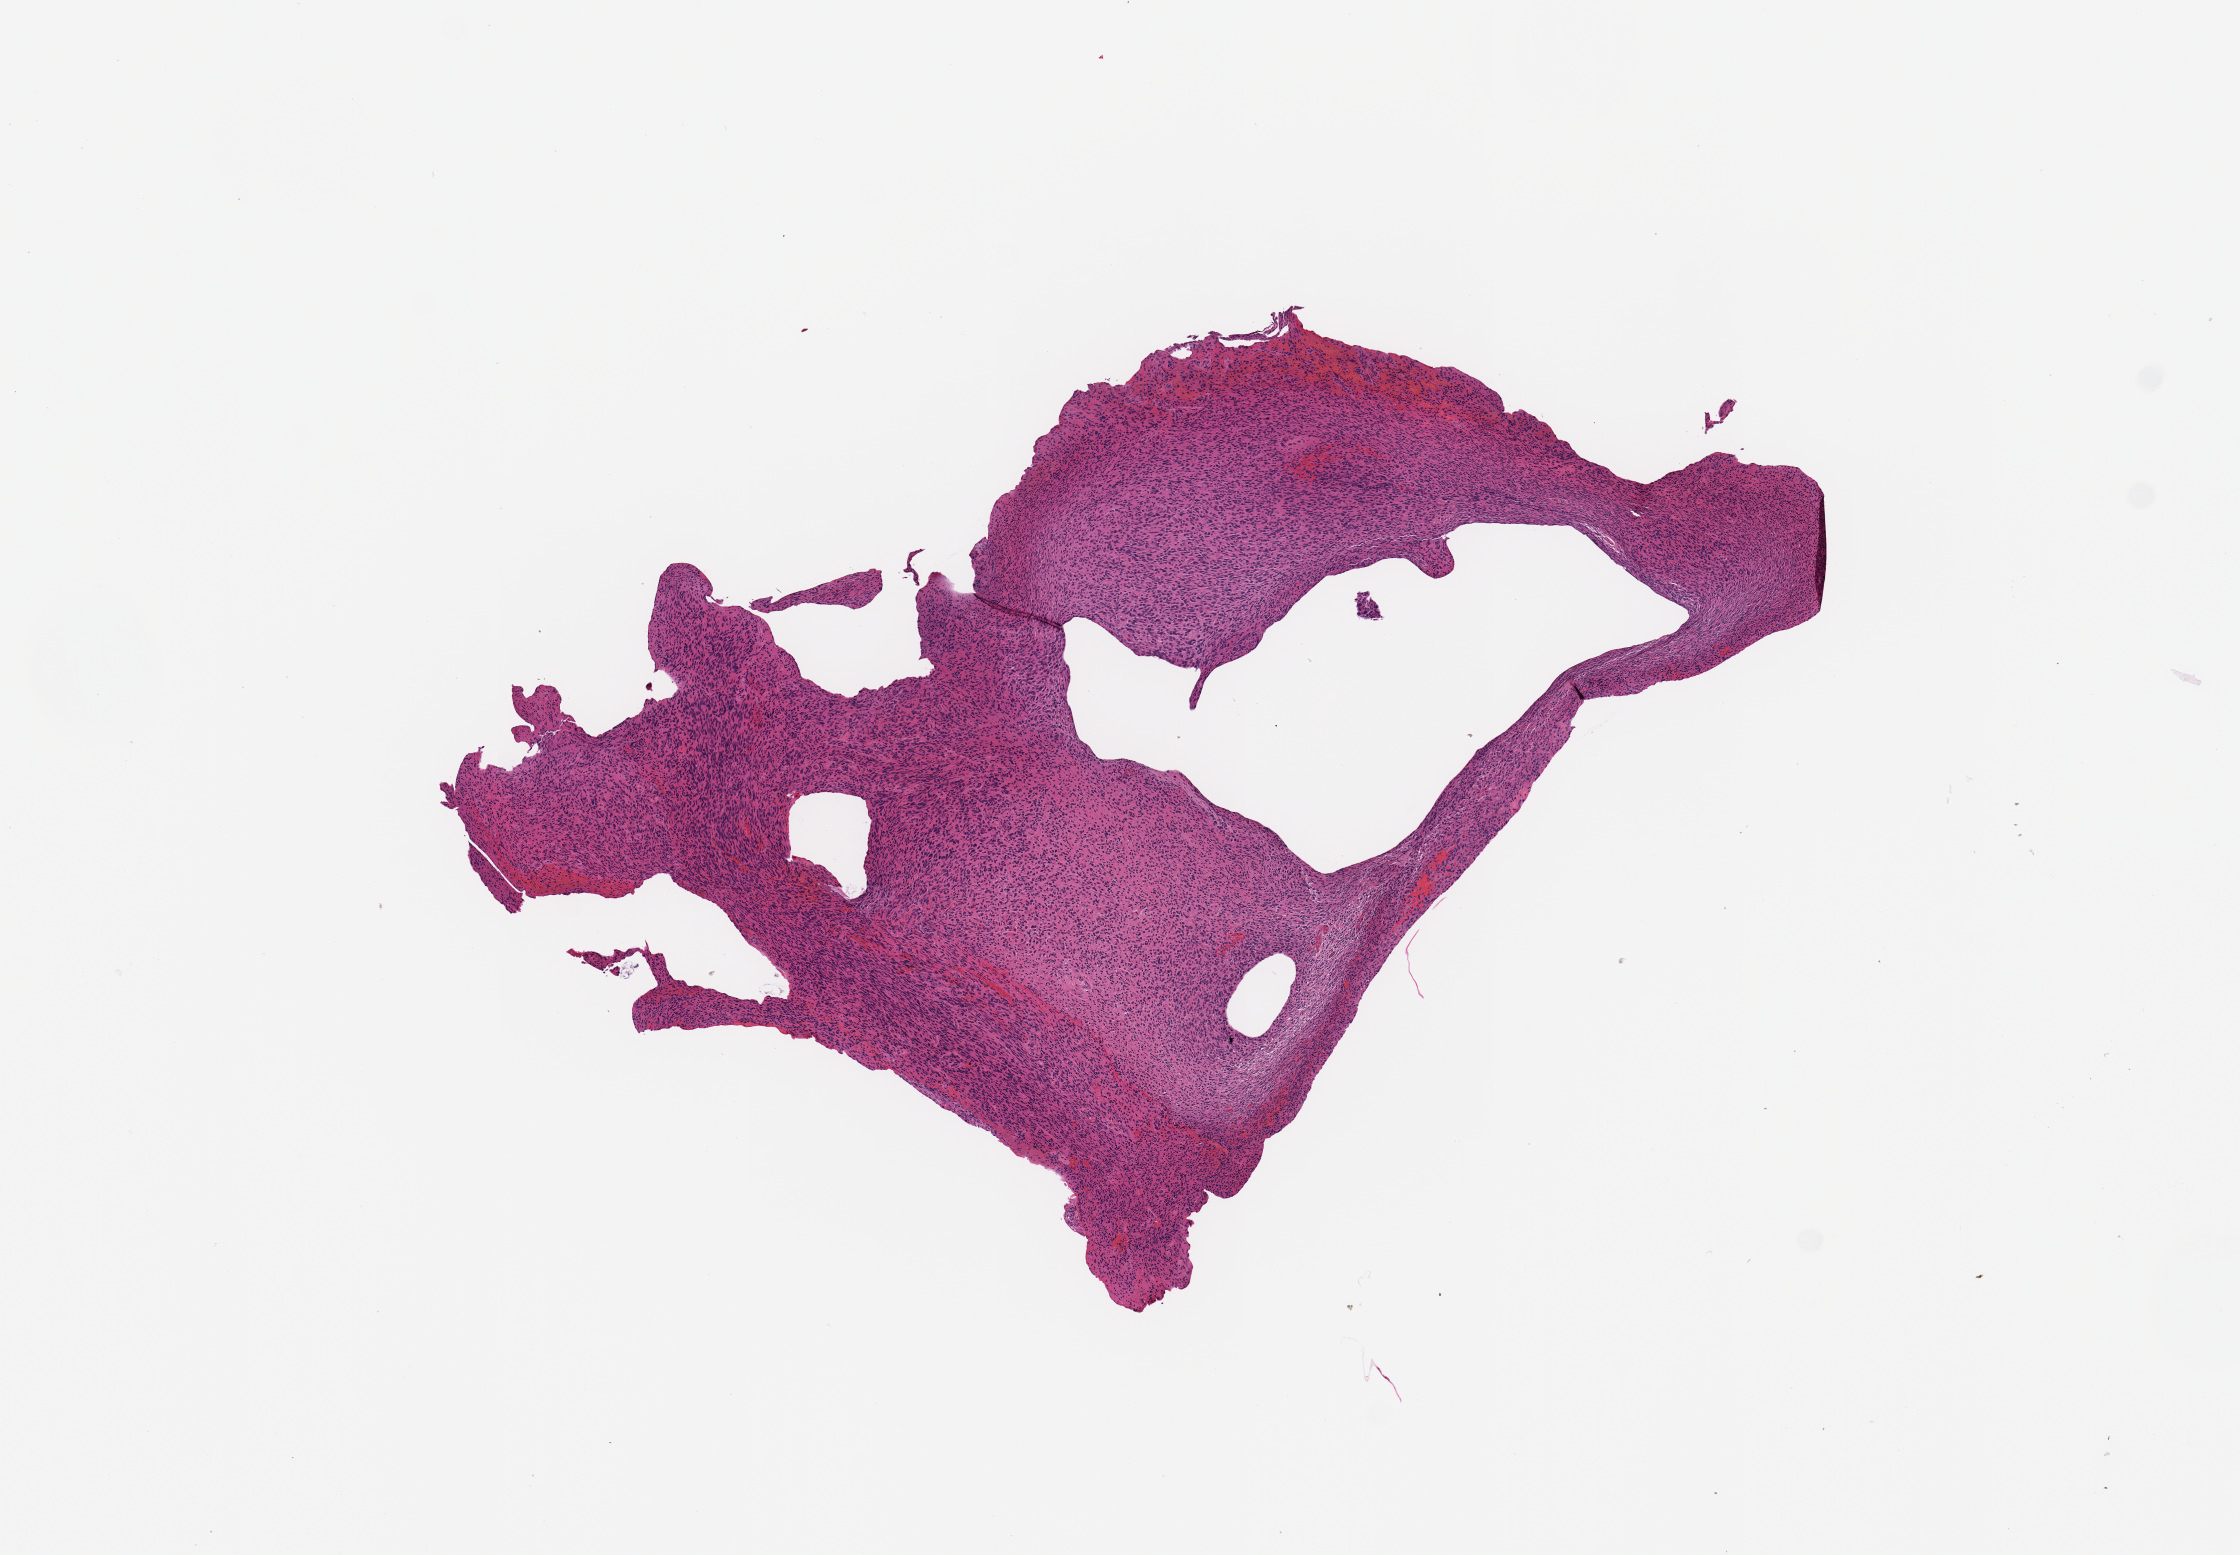
Hematoxylin and eosin (H&E) stained whole-slide image, shown as a low-resolution overview of the whole scanned area (about 8.9 x 6.2 mm). Tumour tissue sample, sampled site: frontal lobe. Male, 66 y/o. Slide review estimates, as recorded: tumour nuclei 90%, necrosis 0%.
Histologic diagnosis: Glioblastoma.